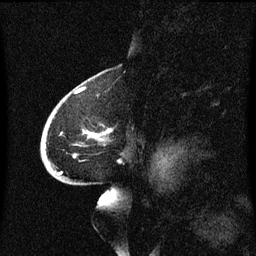
Breast MRI (dynamic contrast-enhanced), one sagittal slice. Dynamic contrast-enhanced series, image 2 of 3 at this slice position (ordered by acquisition). 1.5 T. TE 4.2 ms, TR 8.4 ms. 256 × 256 image matrix. Female patient, age 68 years. Case-level facts recorded for this patient, not image findings: setting: breast cancer imaged before/during neoadjuvant chemotherapy; receptor status: triple-negative.
Structures marked on this image (semi-automatic segmentation, software-assisted and operator-edited):
- analysis volume of interest (the breast-tissue region the enhancement analysis was run in; not a lesion): bounding box [x1, y1, x2, y2] px = [42, 94, 127, 173]
- tumour enhancement mask (voxels above the 70 % enhancement threshold inside the analysis volume of interest): [44, 130, 113, 173]